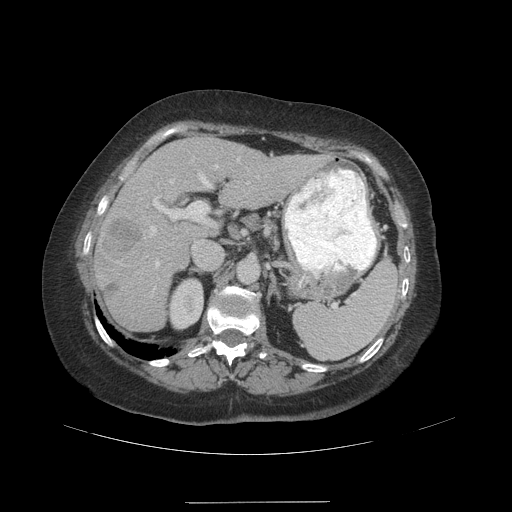
Contrast-enhanced abdominal CT (liver protocol), one axial slice; reconstruction kernel STANDARD; 140 kVp; soft-tissue window (W 400 / L 40 HU); 2.5 mm slice thickness; 512 × 512 image matrix, field of view 440 × 440 mm. From the clinical record (not read from this slice): diagnosis: hepatocellular carcinoma (patient treated with transarterial chemoembolisation; whether this scan precedes or follows treatment is not stated here); TNM stage (as recorded): Stage-IVA; Child-Pugh class: A; tumour nodularity: multinodular.
Structures marked on this image (semi-automatic segmentation, software-assisted and operator-edited):
- liver parenchyma outside the tumour (the mass and vessels are separate outlines, so this box may not span the whole liver): bounding box <94,136,325,330> (left, top, right, bottom; pixels)
- mass: <102,217,142,300>
- liver vessels: <150,158,250,267>